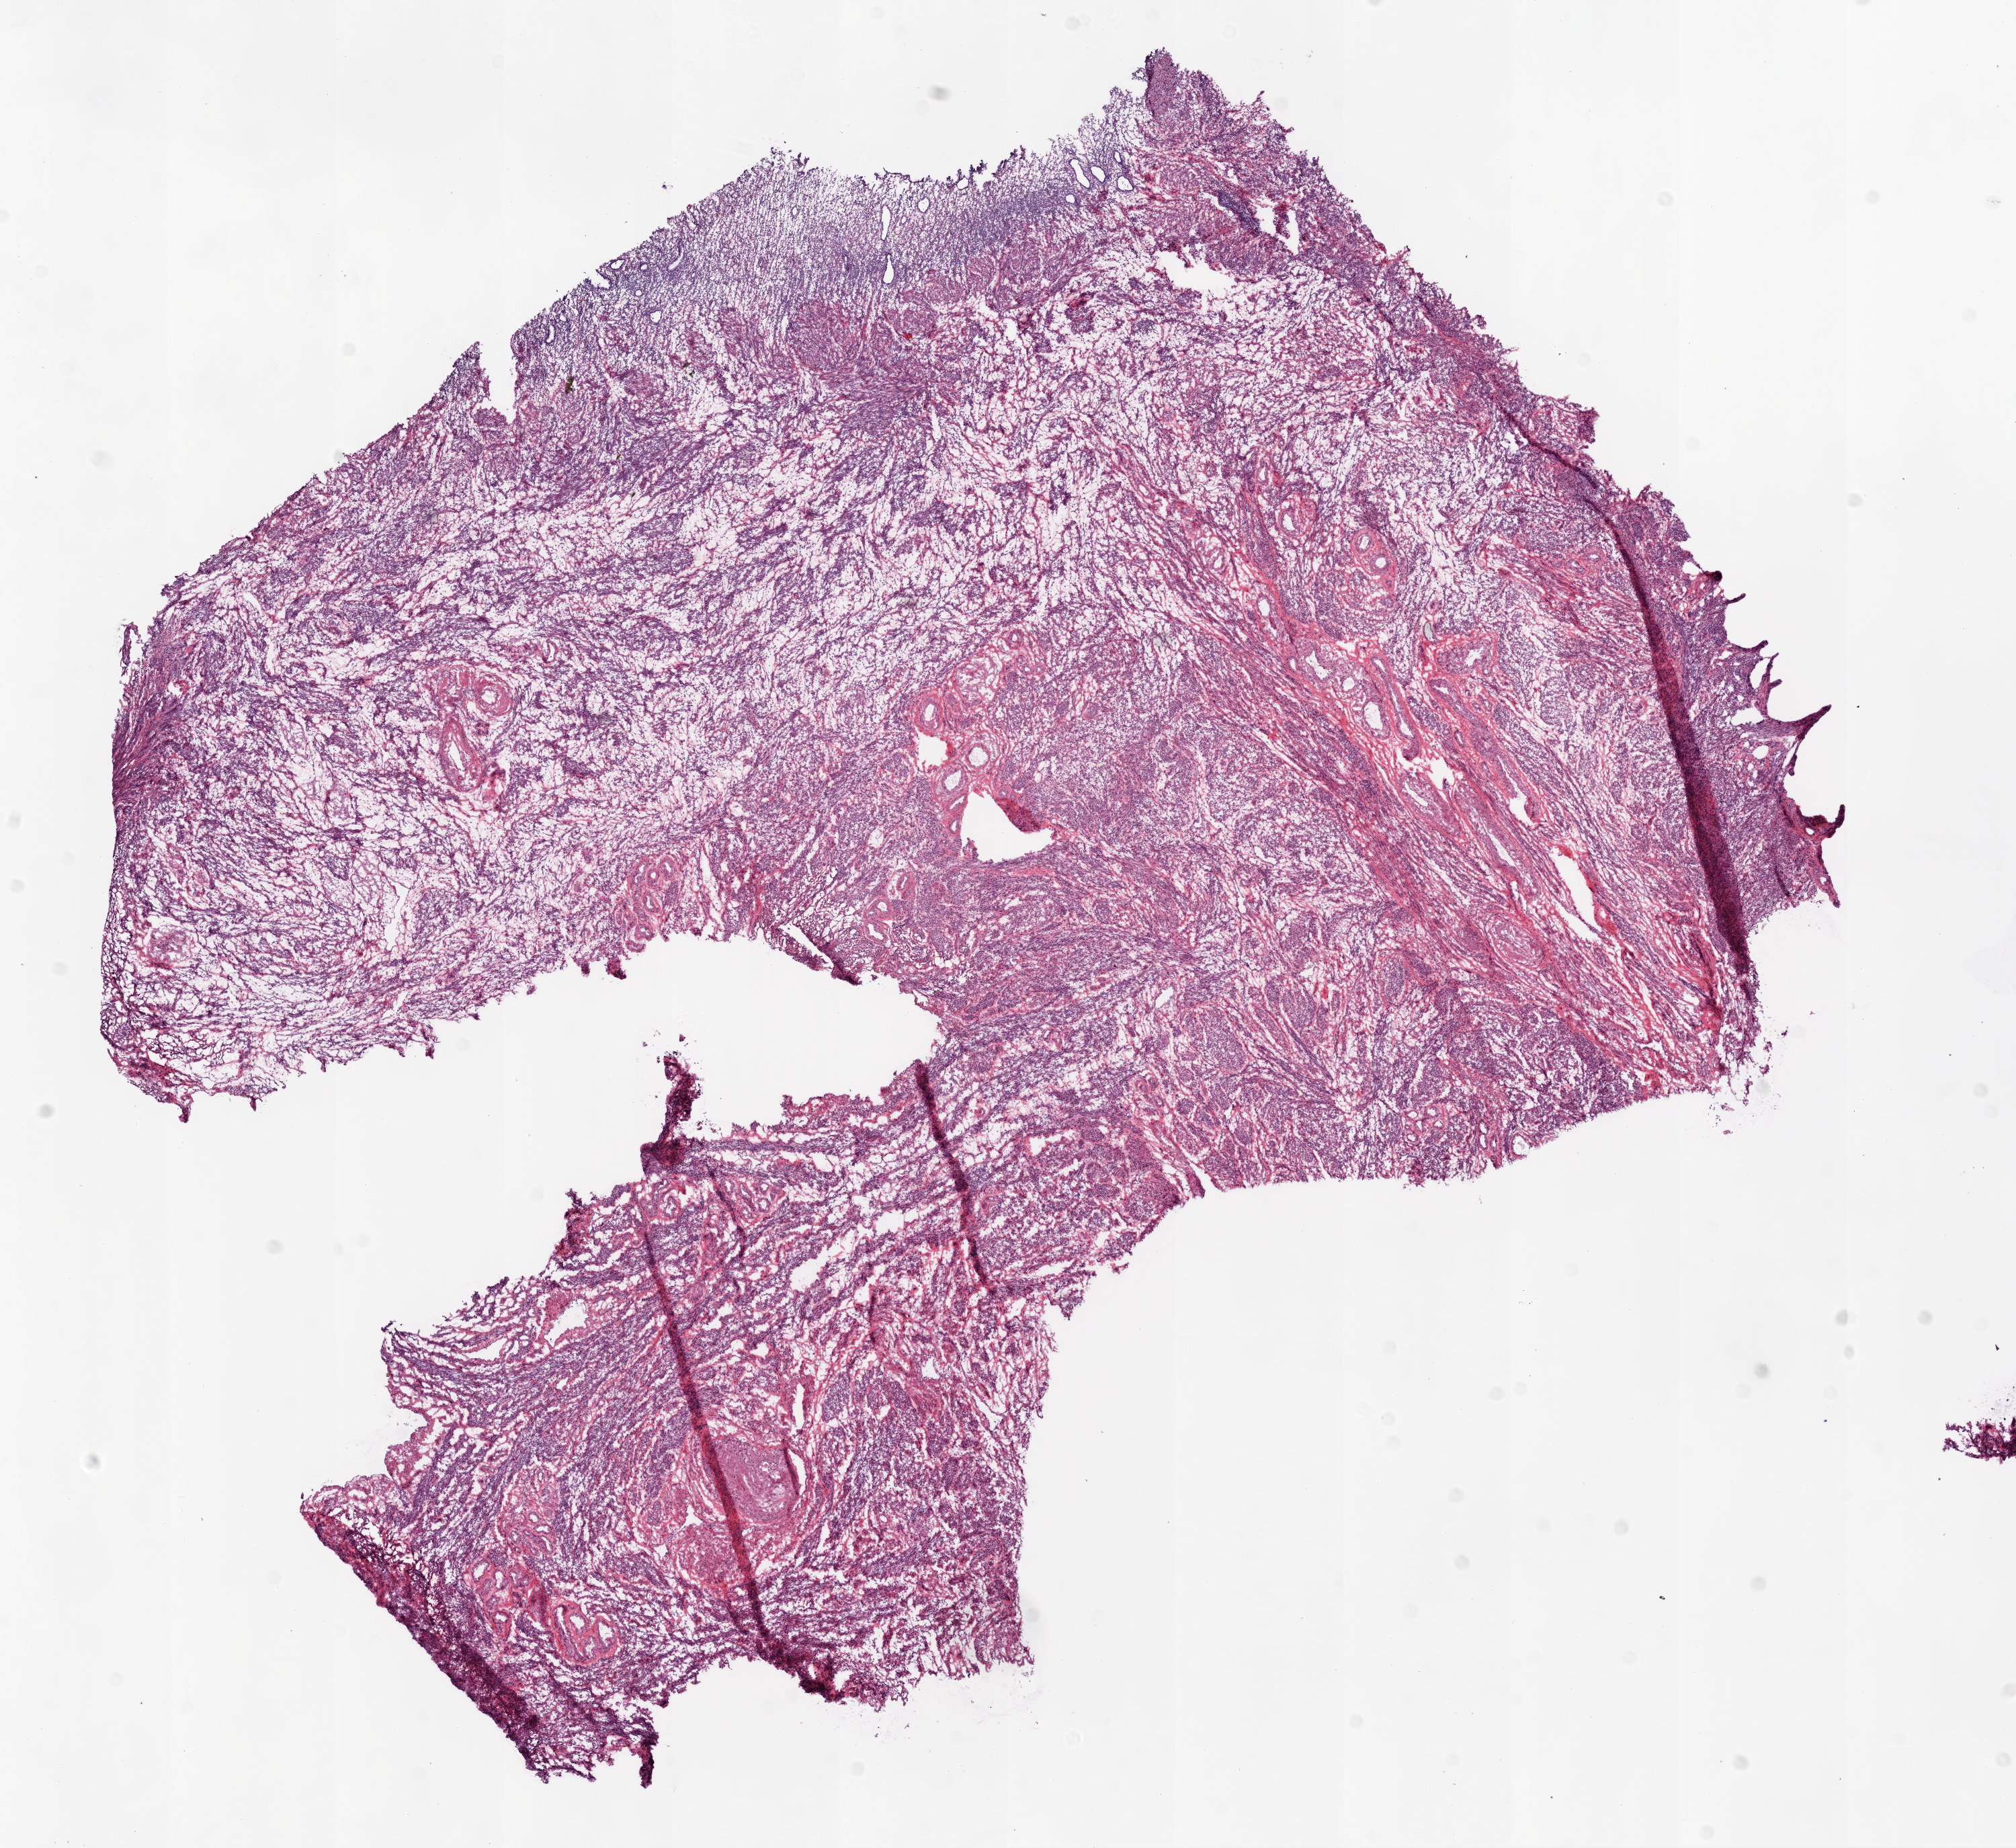
Whole-slide histology image, Hematoxylin and eosin (H&E) stained — shown as a low-resolution overview of the whole scanned area (about 12.0 x 11.0 mm). Frozen section. Solid tissue normal (non-tumour tissue) sample from the ovary. Female, age 62 years at initial diagnosis.
This section: solid tissue normal (non-tumour) sample from the same patient. Patient diagnosis: Serous cystadenocarcinoma, NOS.